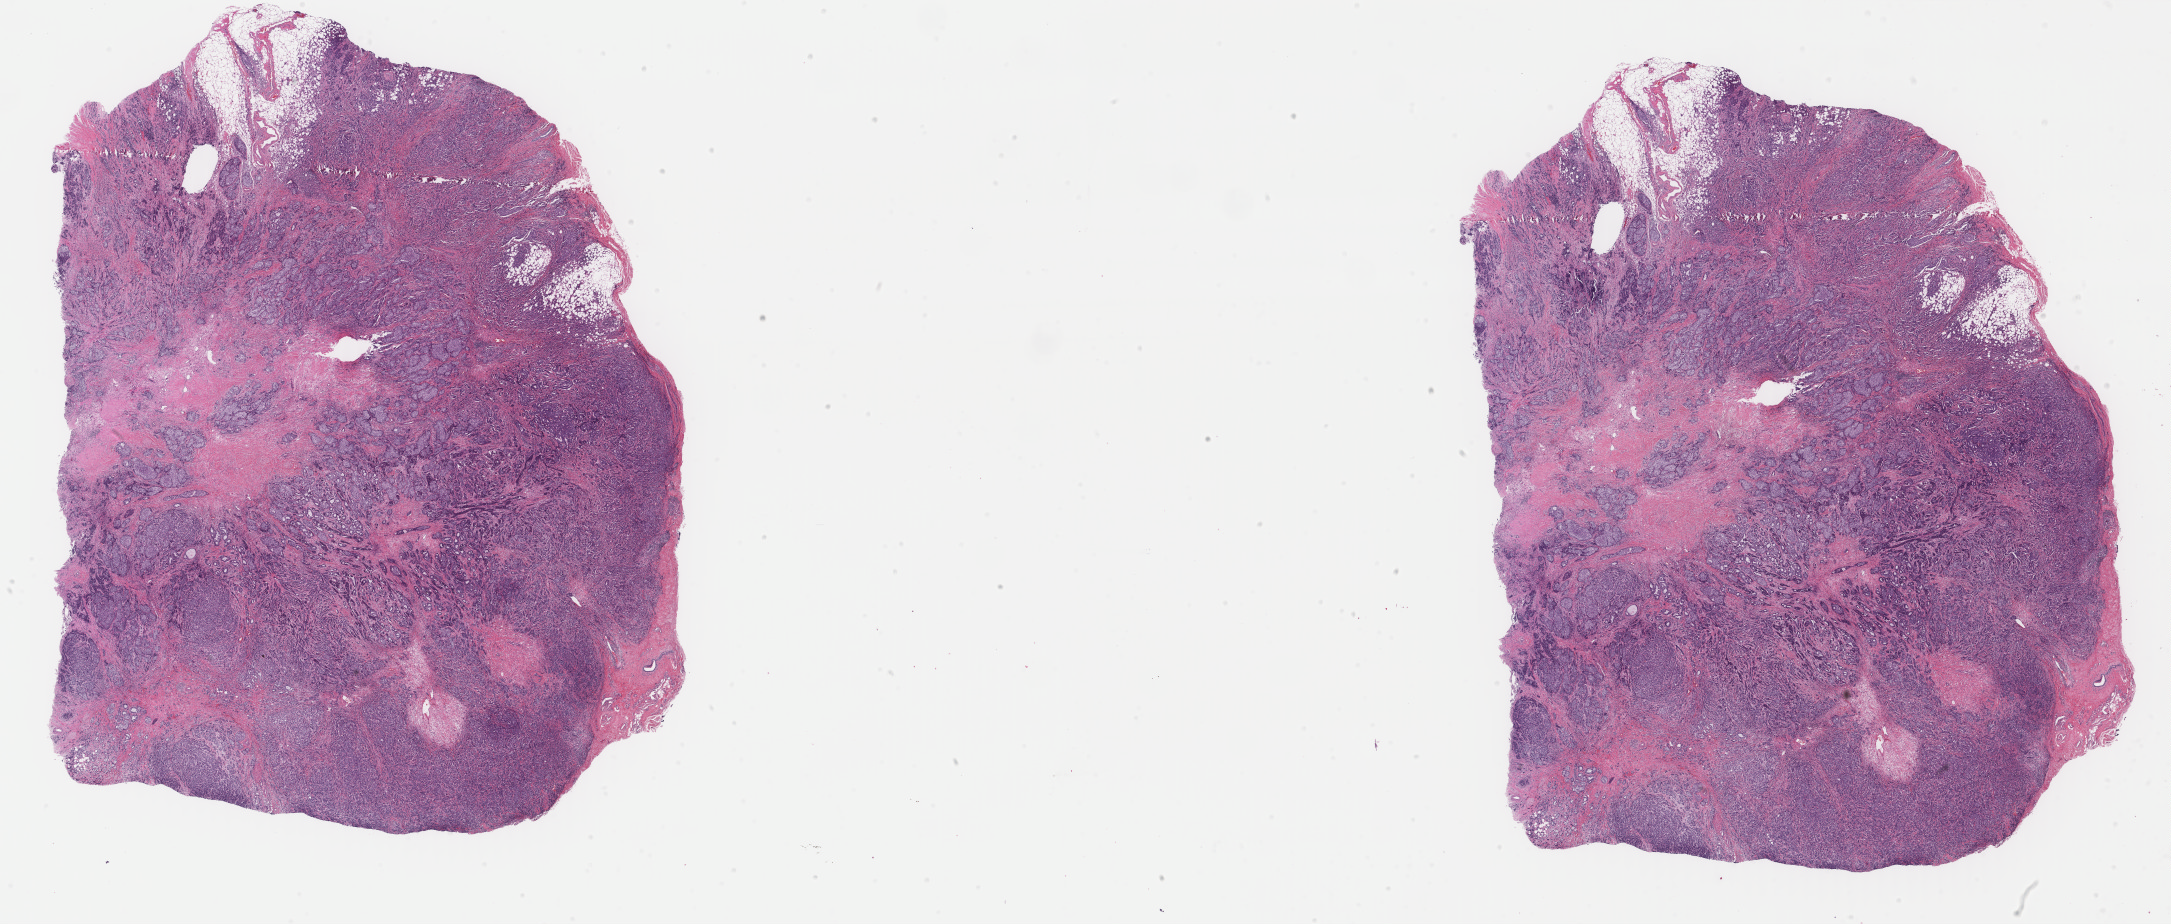
H&E whole-slide image, shown as a low-resolution overview of the whole scanned area (about 34.5 x 14.7 mm, acquisition: 40x scan). FFPE section. Primary tumour sample from the breast. Patient: female, age at initial diagnosis 32 years.
AJCC pathologic stage: IA. Lymph nodes positive (case pathology): 0 of 14 examined. Histologic diagnosis: Infiltrating duct carcinoma, NOS.